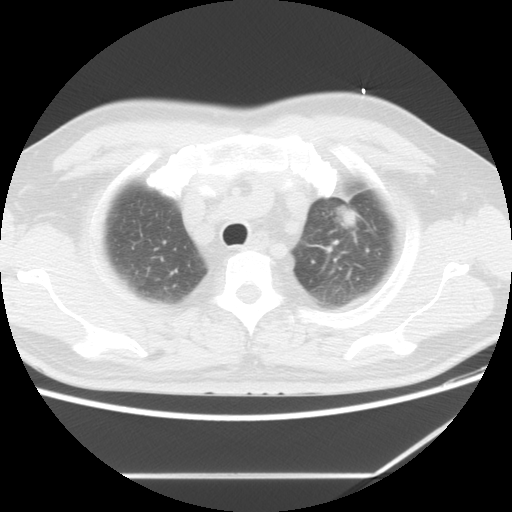
Chest CT, one axial slice; position 11 of 13 along the scan axis; reconstruction kernel STANDARD; 120 kVp; lung window (W 1500 / L -600 HU); 5 mm slice thickness; 512 × 512 image matrix. Patient: male, 56 years. Case-level facts recorded for this patient, not image findings: clinical TNM (as recorded): T2 N3 M1.
Structures marked on this image (rectangle marked by the reading radiologist):
- lung tumour (recorded histology: adenocarcinoma): bounding box (x1, y1, x2, y2) in pixels: (343, 208, 360, 226)